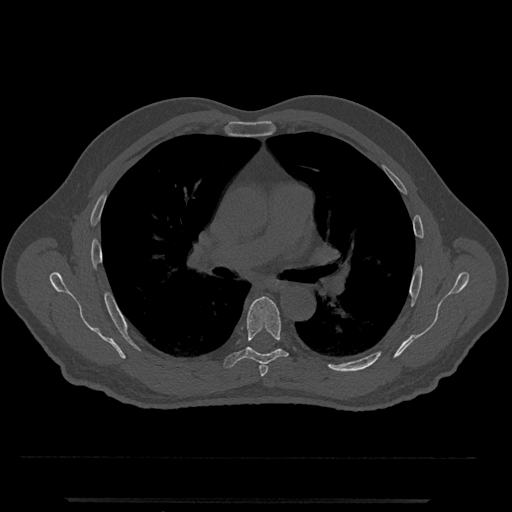
CT including the spine, one axial slice. Position 742 of 797 along the scan axis. 120 kVp. Bone window (W 1800 / L 400 HU). 0.5 mm slice thickness. 512 × 512 image matrix, field of view 419 × 419 mm. Male patient, age 63 years. From the clinical record (not read from this slice): primary cancer: prostate.
Outlined on this slice (semi-automatically segmented with operator editing):
- T5 vertebra: bounding box [x1, y1, x2, y2] px = [259, 364, 268, 377]
- T6 vertebra: [224, 296, 289, 368]